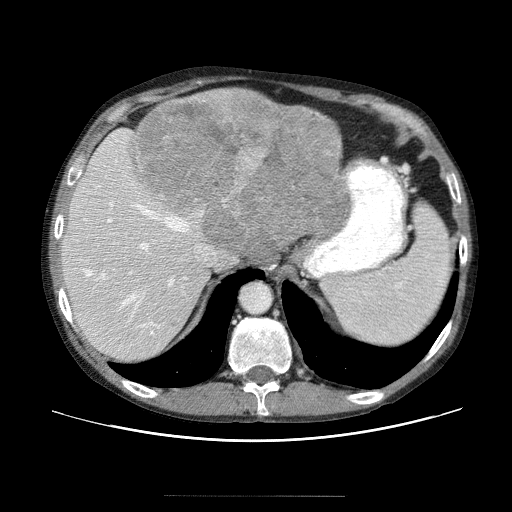
Contrast-enhanced abdominal CT (liver protocol), one axial slice; slice 43 of 69 in the series (ordered by position); reconstruction kernel STANDARD; 120 kVp; soft-tissue window (W 400 / L 40 HU); 2.5 mm slice thickness; 512 × 512 image matrix, field of view 380 × 380 mm. From the clinical record (not read from this slice): diagnosis: hepatocellular carcinoma (patient treated with transarterial chemoembolisation; whether this scan precedes or follows treatment is not stated here); TNM stage (as recorded): Stage-IVB; Child-Pugh class: B; tumour differentiation: poorly differentiated; tumour nodularity: multinodular.
Outlined on this slice (semi-automatically segmented with operator editing):
- liver parenchyma outside the tumour (the mass and vessels are separate outlines, so this box may not span the whole liver): bounding box (x1, y1, x2, y2) in pixels: (61, 100, 342, 364)
- mass: (132, 86, 346, 268)
- liver vessels: (89, 153, 205, 332)